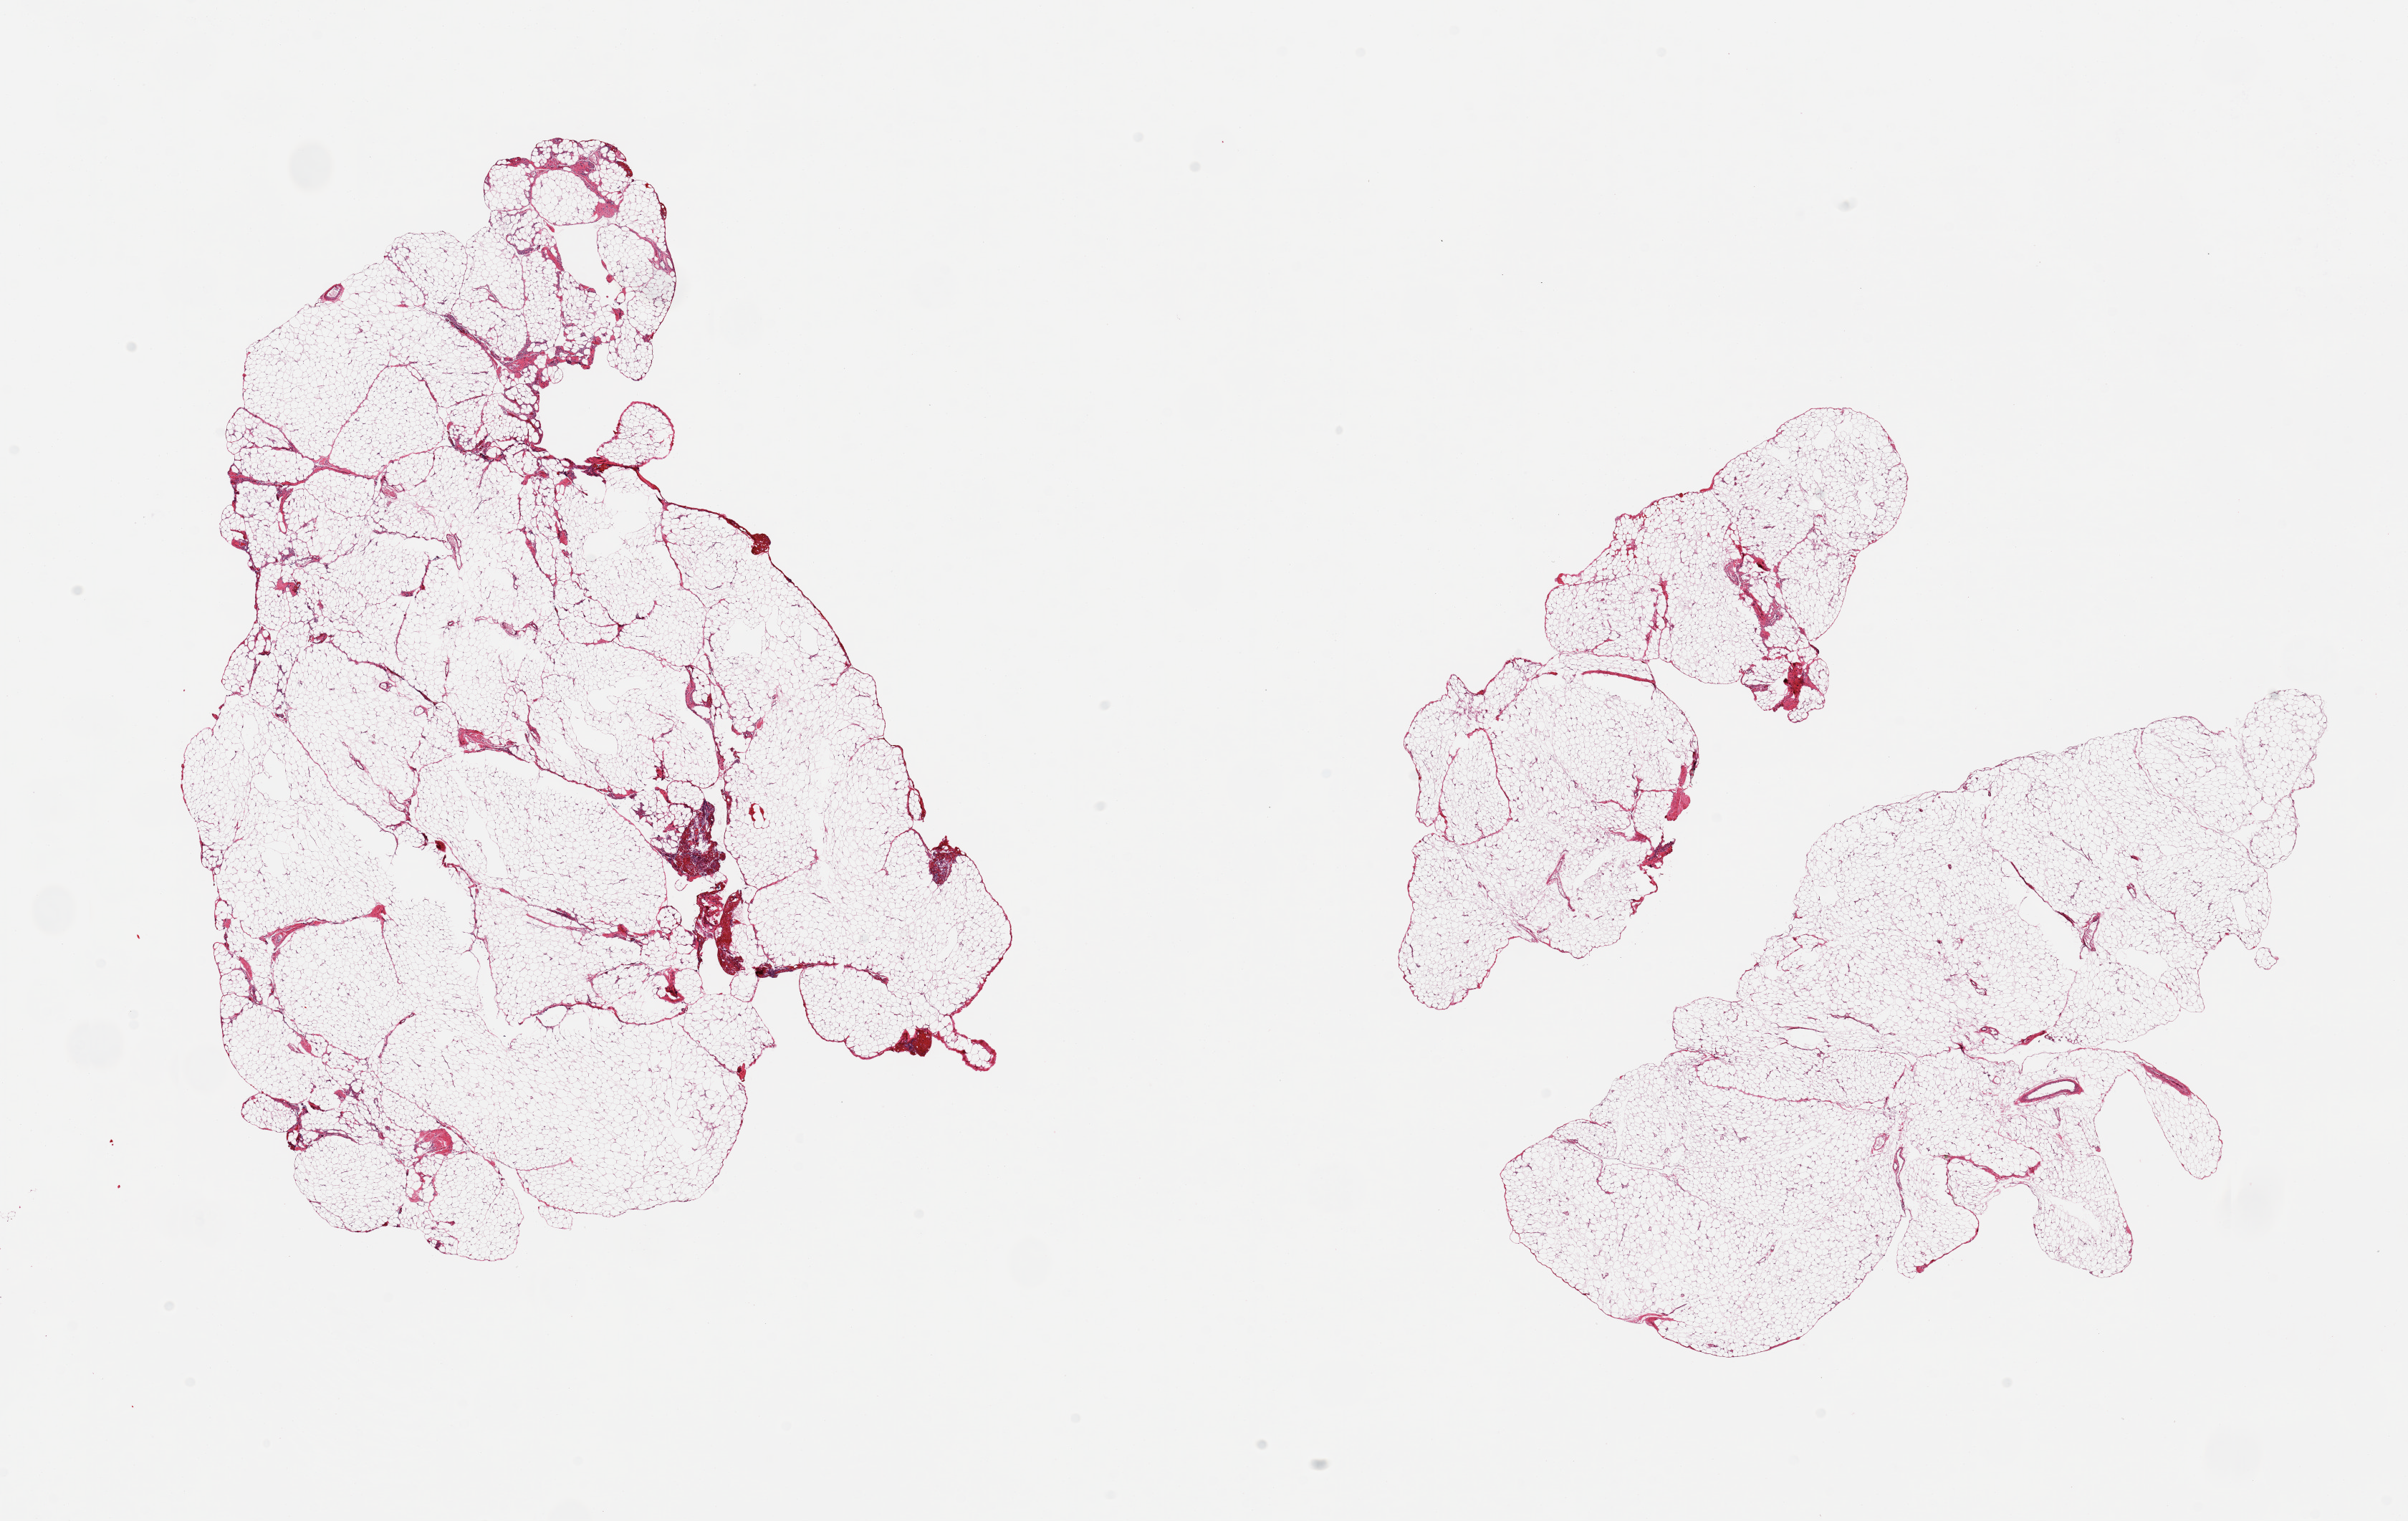
Hematoxylin and eosin (H&E) whole-slide image — low-resolution overview of the scanned area, about 26.6 x 16.8 mm, PAXgene-fixed, paraffin-embedded tissue, target tissue: omentum, tissue donor sample. Female donor.
Reviewer comment on this tissue sample: 2 pieces, minimal fibrosis.